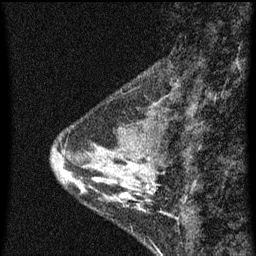
Breast MRI (dynamic contrast-enhanced), one sagittal slice; position 21 of 60 along the scan axis; dynamic contrast-enhanced series, image 2 of 3 at this slice position (ordered by acquisition); 1.5 T; TE 4.2 ms, TR 8 ms; 256 × 256 image matrix, field of view 180 × 180 mm. Female patient, age 34 years.
Outlined on this slice (semi-automatically segmented with operator editing):
- analysis volume of interest (the breast-tissue region the enhancement analysis was run in; not a lesion): bounding box <70,138,157,211> (left, top, right, bottom; pixels)
- tumour enhancement mask (voxels above the 70 % enhancement threshold inside the analysis volume of interest): <122,186,149,197>